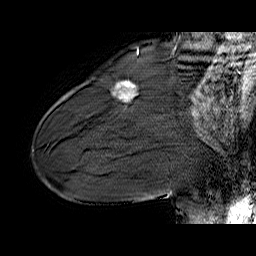
Breast MRI (dynamic contrast-enhanced), one sagittal slice; position 19 of 60 along the scan axis; dynamic contrast-enhanced series, time point 2 of 6 at this slice position (early post-contrast); 1.5 T; TE 6.4 ms, TR 32.9 ms; 4 mm slice thickness; 256 × 256 image matrix, field of view 200 × 200 mm. Female patient. From the clinical record (not read from this slice): setting: breast cancer imaged before/during neoadjuvant chemotherapy; receptor status: HER2-positive.
Outlined on this slice (semi-automatic segmentation, software-assisted and operator-edited):
- analysis volume of interest (the breast-tissue region the enhancement analysis was run in; not a lesion): box from (x=114, y=81) to (x=138, y=102) px
- tumour enhancement mask (voxels above the 100 % enhancement threshold inside the analysis volume of interest): (x=132, y=86)–(x=134, y=88)